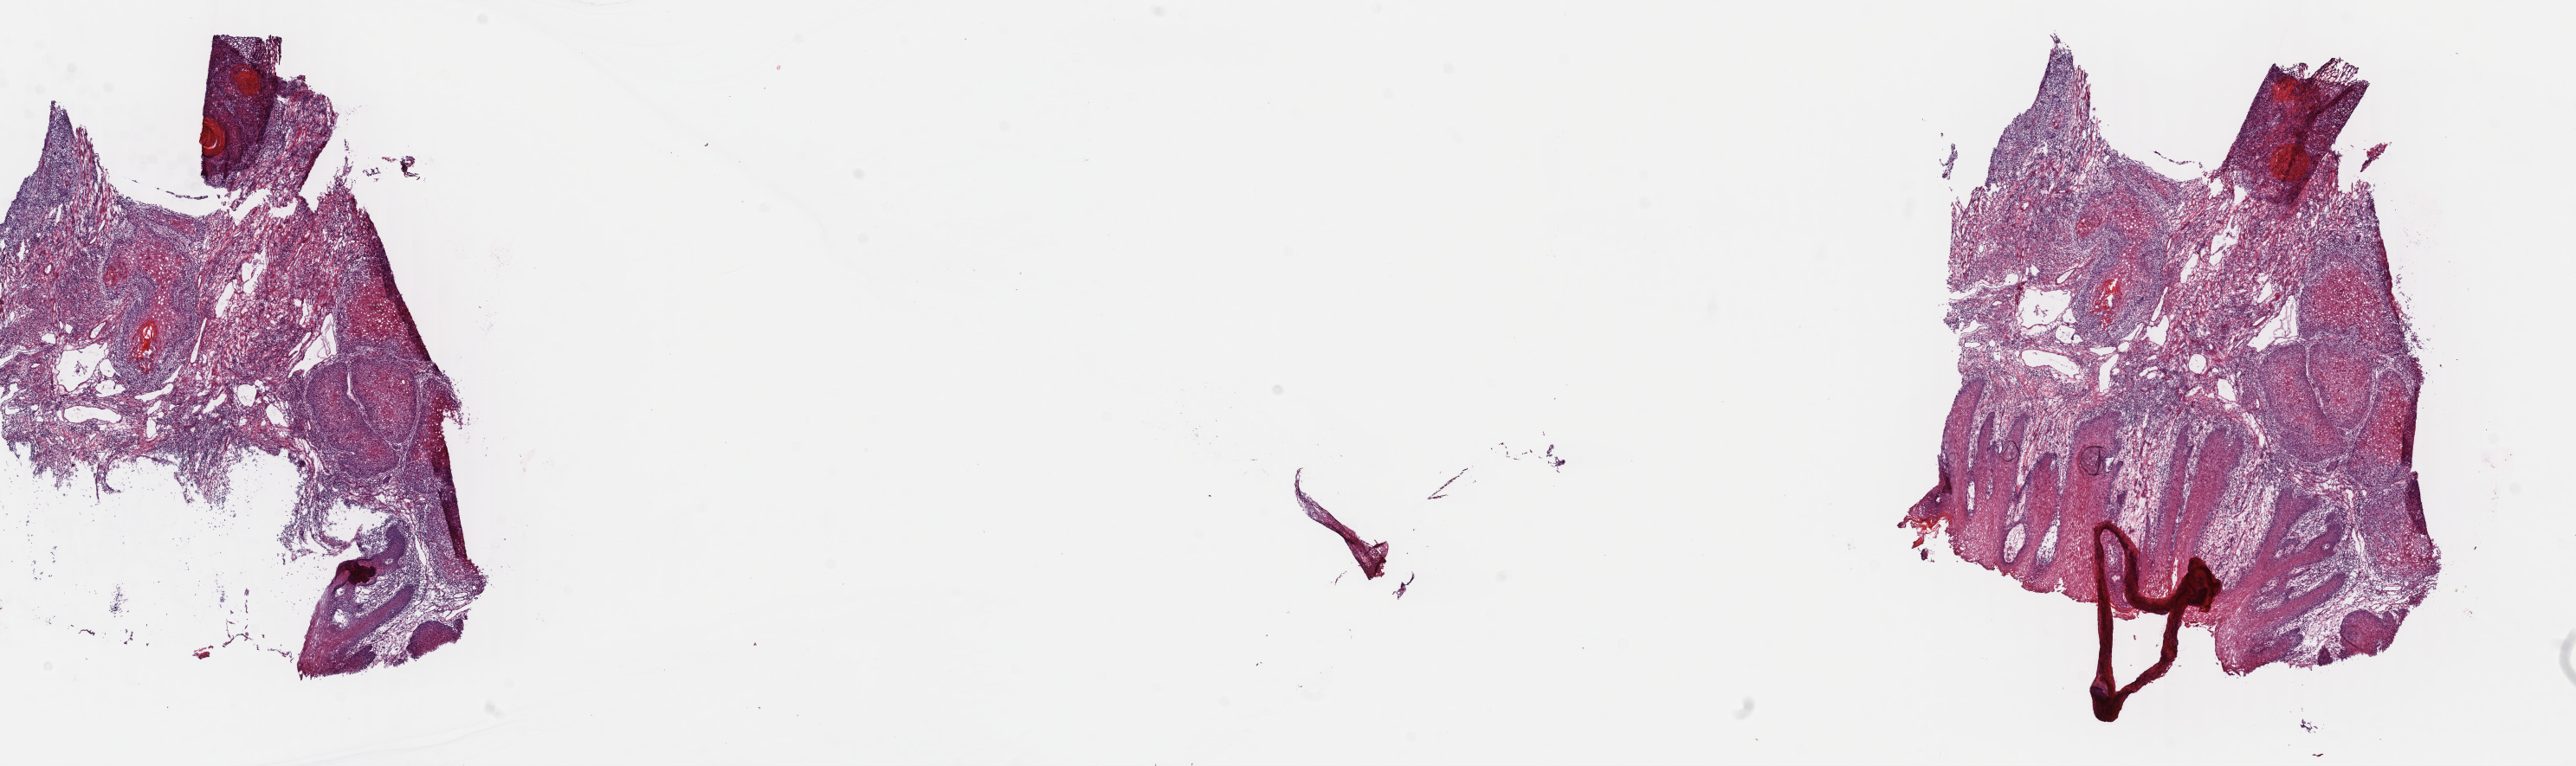
H&E whole-slide image — low-resolution overview of the scanned area, about 23.4 x 7.0 mm (slide scanned at 40x); frozen section from the top of the tissue portion; head and neck, primary tumour sample. Patient: male, age at initial diagnosis 66 years. Composition of this section per pathologist review: tumour cells 60%, tumour nuclei 75%.
Diagnosis: Squamous cell carcinoma, NOS (tongue, NOS).